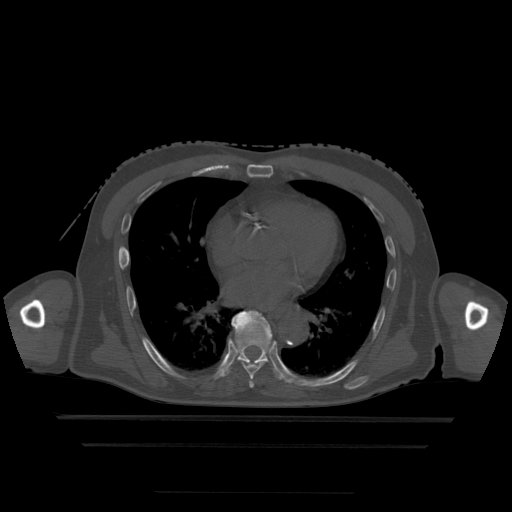
CT including the spine, one axial slice. Slice 290 of 522 in the series (ordered by position). Bone window (W 1800 / L 400 HU). 512 × 512 image matrix. Patient age 68 years. Case-level facts recorded for this patient, not image findings: primary cancer: urothelial.
Annotated regions visible in this slice (semi-automatic segmentation, software-assisted and operator-edited):
- T6 vertebra: bounding box <249,380,255,388> (left, top, right, bottom; pixels)
- T7 vertebra: <243,362,264,380>
- T8 vertebra: <223,311,283,380>